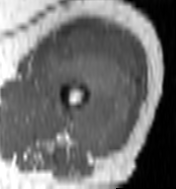
MRI of an extremity soft-tissue mass, one axial slice. Slice 69 of 100 in the series (ordered by position). MR volume resampled by the dataset authors to the PET/CT grid (not the native acquisition matrix). 176 × 189 image matrix, field of view 172 × 185 mm. Female patient. From the clinical record (not read from this slice): histological type: undifferentiated – high grade; grade: high; site of the primary tumour: left thigh.
Structures marked on this image (expert contour drawn on MRI and transferred to this co-registered scan by the dataset authors):
- gross tumour volume including surrounding oedema: bounding box <44,29,138,158> (left, top, right, bottom; pixels)
- gross tumour volume (mass): <44,29,138,158>